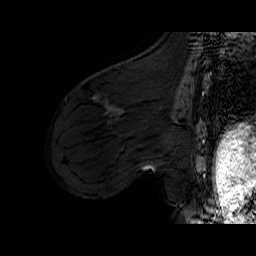
Breast MRI (dynamic contrast-enhanced), one sagittal slice. Slice 24 of 60 in the series (ordered by position). Dynamic contrast-enhanced series, time point 2 of 6 at this slice position (early post-contrast). 1.5 T. TE 6.4 ms, TR 32.9 ms. 256 × 256 image matrix, field of view 200 × 200 mm. Female patient. From the clinical record (not read from this slice): setting: breast cancer imaged before/during neoadjuvant chemotherapy; receptor status: HER2-positive.
Outlined on this slice (semi-automatic segmentation, software-assisted and operator-edited):
- analysis volume of interest (the breast-tissue region the enhancement analysis was run in; not a lesion): bounding box [x1, y1, x2, y2] px = [78, 94, 152, 149]
- tumour enhancement mask (voxels above the 100 % enhancement threshold inside the analysis volume of interest): [93, 96, 96, 98]